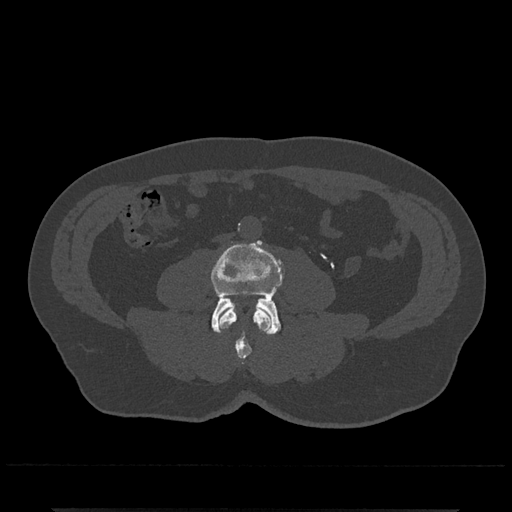
CT including the spine, one axial slice. Slice 182 of 797 in the series (ordered by position). Reconstruction kernel Br40s/3. 120 kVp. Bone window (W 1800 / L 400 HU). 512 × 512 image matrix, field of view 393 × 393 mm. Male patient, age 67 years. Case-level facts recorded for this patient, not image findings: primary cancer: prostate.
Structures marked on this image (semi-automatic segmentation, software-assisted and operator-edited):
- L3 vertebra: bounding box [x1, y1, x2, y2] px = [218, 307, 272, 364]
- L4 vertebra: [211, 241, 284, 335]